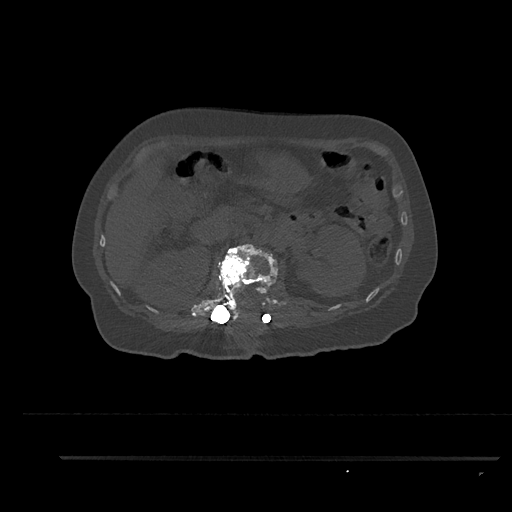
CT including the spine, one axial slice; bone window (W 1800 / L 400 HU); 0.5 mm slice thickness; 512 × 512 image matrix, field of view 408 × 408 mm. Patient: female, 44 years. From the clinical record (not read from this slice): primary cancer: renal; vertebrae with lytic lesions (as recorded): L1.
Outlined on this slice (semi-automatically segmented with operator editing):
- L1 vertebra: bounding box (x1, y1, x2, y2) in pixels: (203, 244, 278, 322)